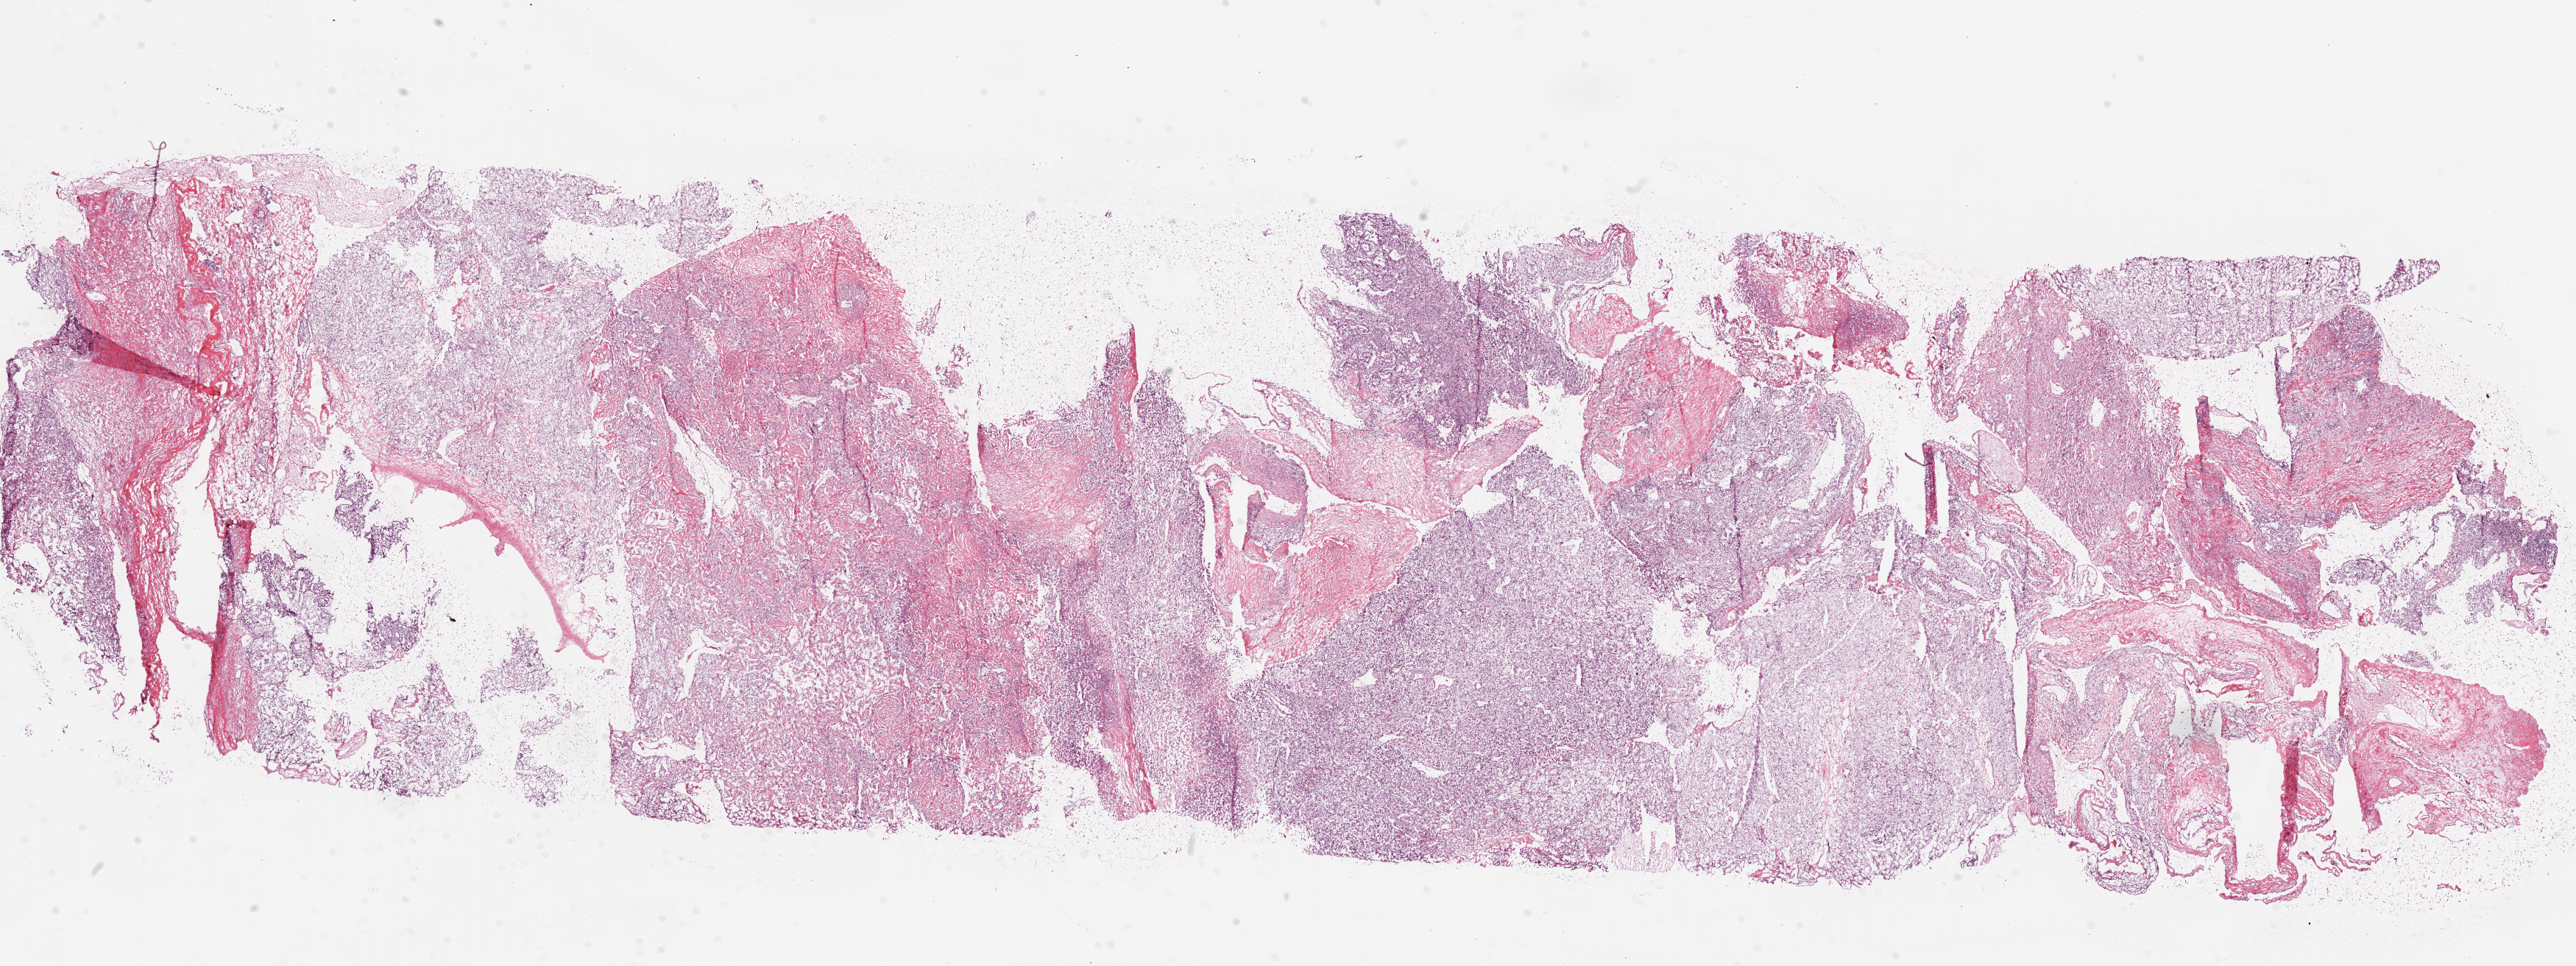
Whole-slide histology image, Hematoxylin and eosin (H&E) stained, a low-resolution overview of the entire scanned area, about 28.1 x 10.5 mm (acquisition: 20x scan), frozen section from the bottom of the tissue portion, sample: primary tumour, kidney. Male, age 42 years at initial diagnosis. Histologic grade: G3 (poorly differentiated). Slide review estimates, as recorded: tumour cells 75%, tumour nuclei 80%, normal cells 0%, stromal cells 25%, necrosis 0%.
Lymph nodes positive (case pathology): 0 of 14 examined. AJCC pathologic stage: IV. Histologic diagnosis: Clear cell adenocarcinoma, NOS. Laterality: left.